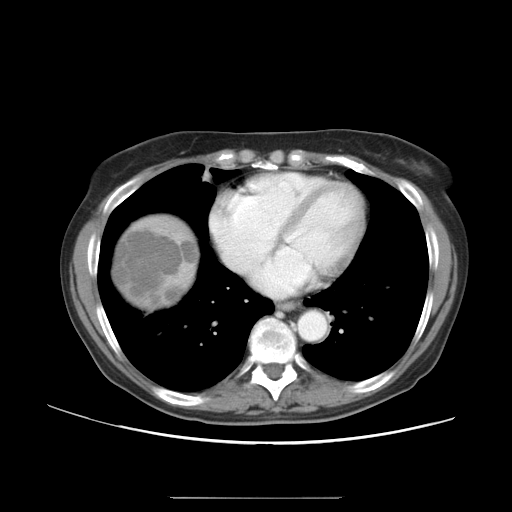
Contrast-enhanced abdominal CT, one axial slice; slice 46 of 50 in the series (ordered by position); reconstruction kernel STANDARD; 120 kVp; soft-tissue window (W 400 / L 40 HU); 512 × 512 image matrix, field of view 389 × 389 mm. Female patient, age 58 years. Case-level facts recorded for this patient, not image findings: diagnosis: colorectal cancer liver metastases, imaged before liver resection; multiple liver metastases: yes; largest metastasis: 7.3 cm; chemotherapy before resection: yes.
Structures marked on this image (manually delineated by an expert):
- liver: box from (x=114, y=218) to (x=196, y=305) px
- liver metastasis: (x=117, y=224)–(x=195, y=301)